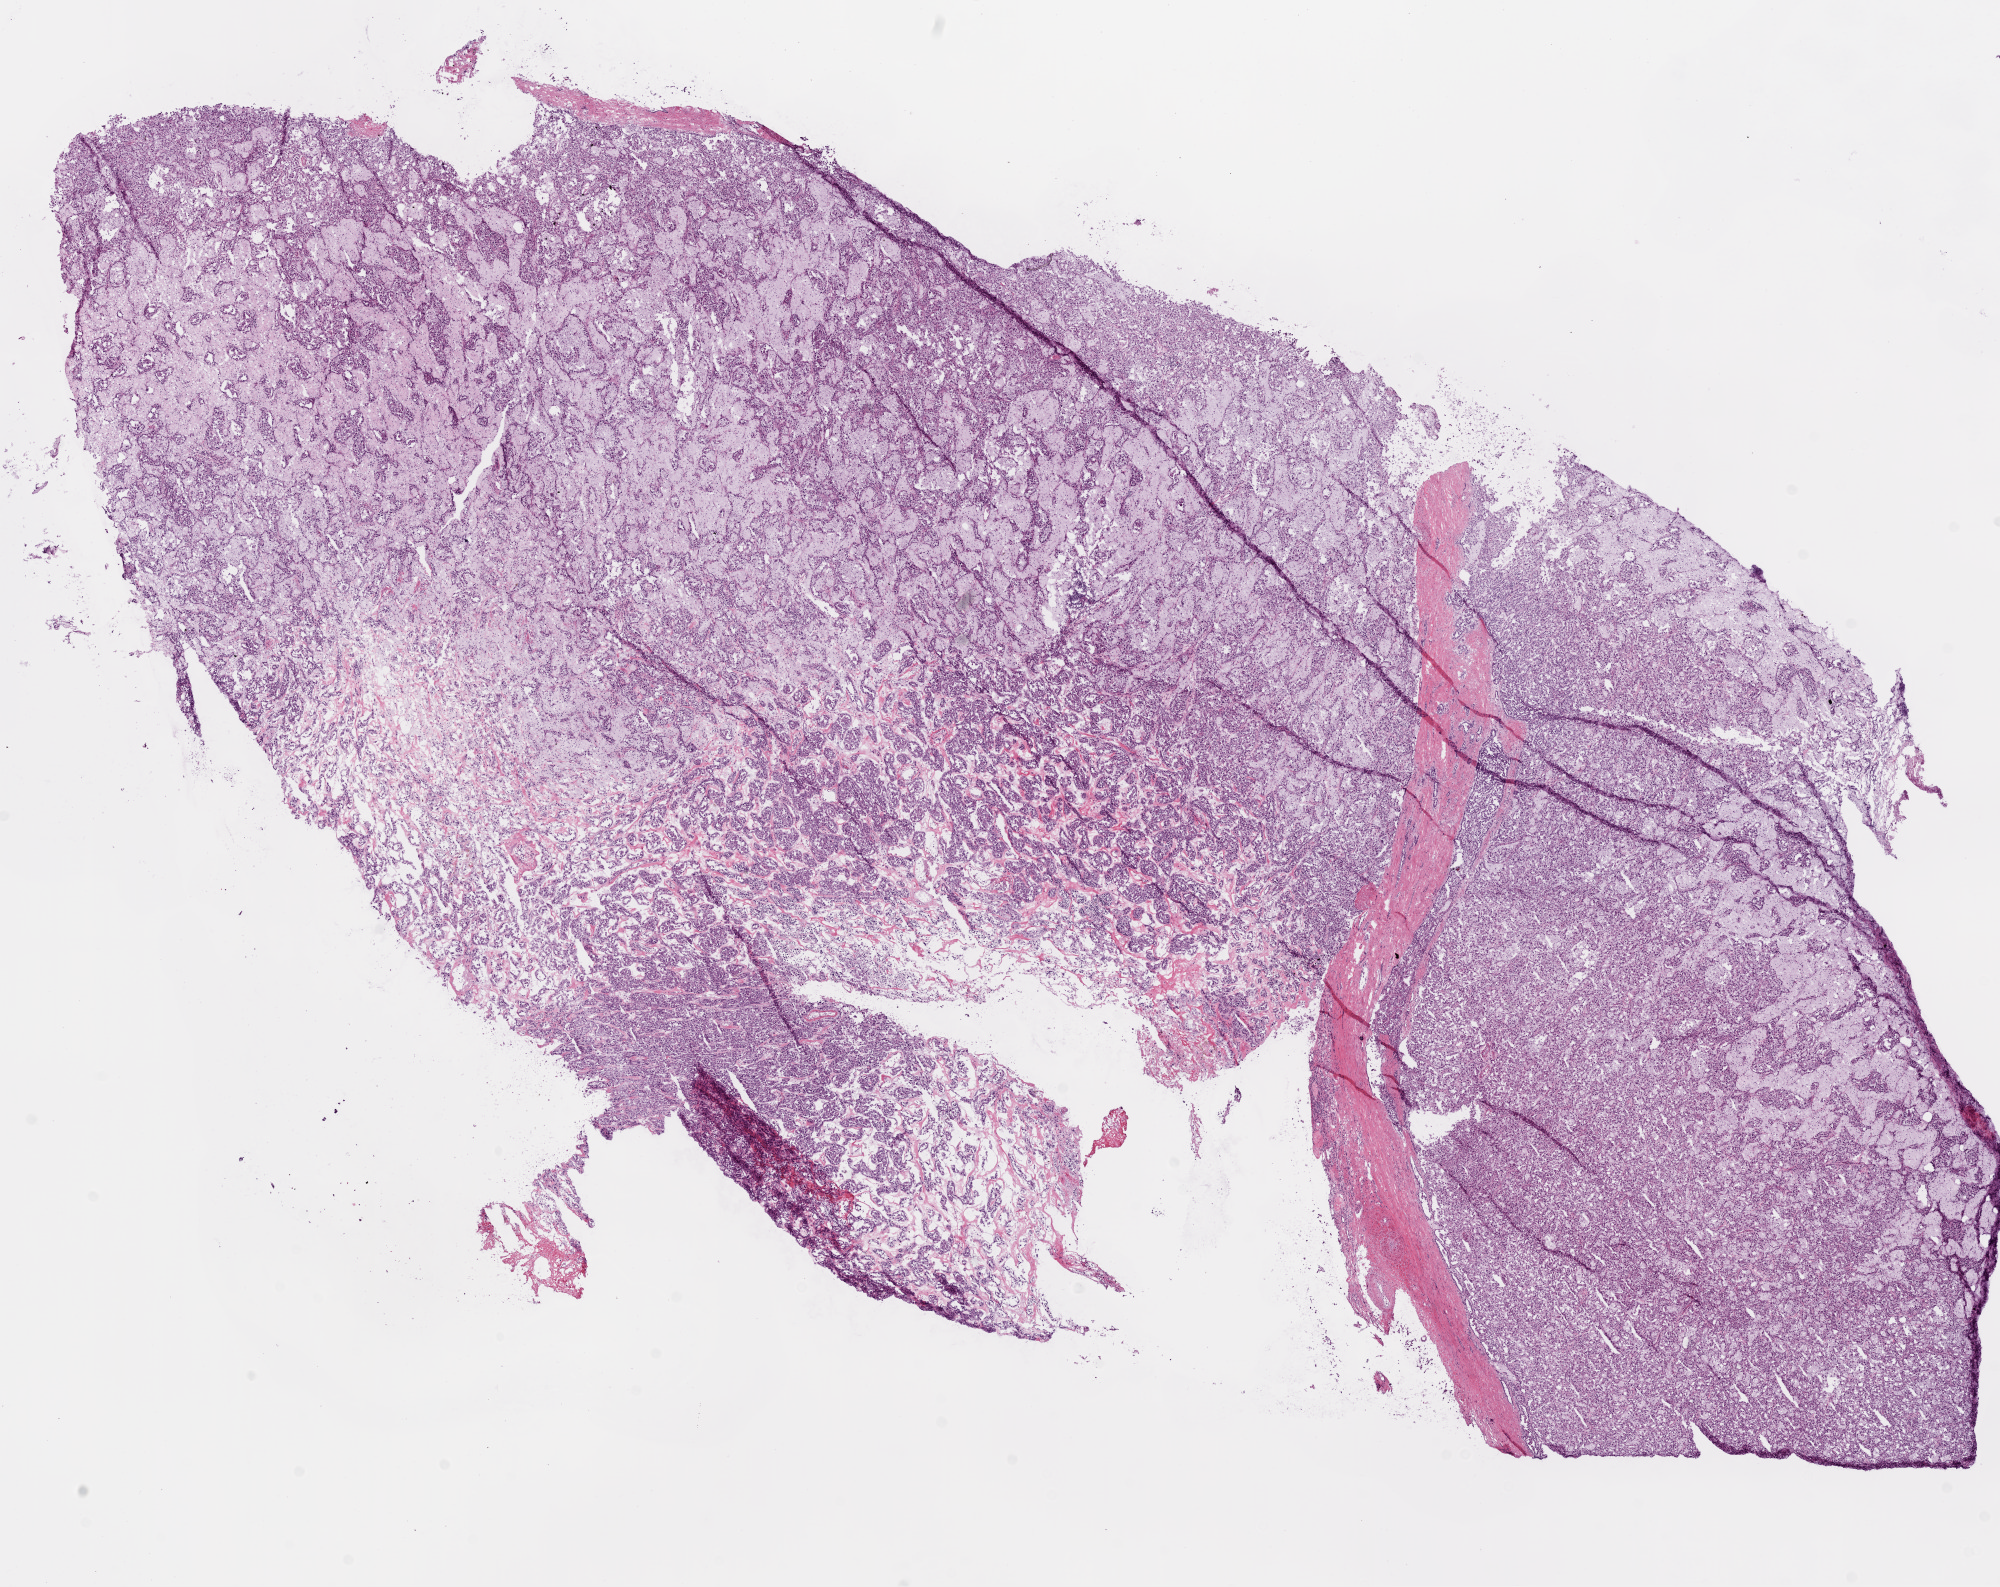
Whole-slide histology image, Hematoxylin and eosin (H&E) stained — shown as a low-resolution overview of the whole scanned area (about 16.0 x 12.7 mm); frozen section; primary tumour sample from the kidney. Female patient; age at initial diagnosis 39 years. Histologic grade: G3 (poorly differentiated). Composition of this section per pathologist review: tumour cells 90%, tumour nuclei 75%, normal cells 0%, stromal cells 10%, necrosis 0%. Inflammatory infiltration, as recorded: lymphocyte infiltration 5%, monocyte infiltration 20%, neutrophil infiltration 0%.
Histologic diagnosis: Clear cell adenocarcinoma, NOS. AJCC pathologic stage: I (6th edition). Laterality: right.